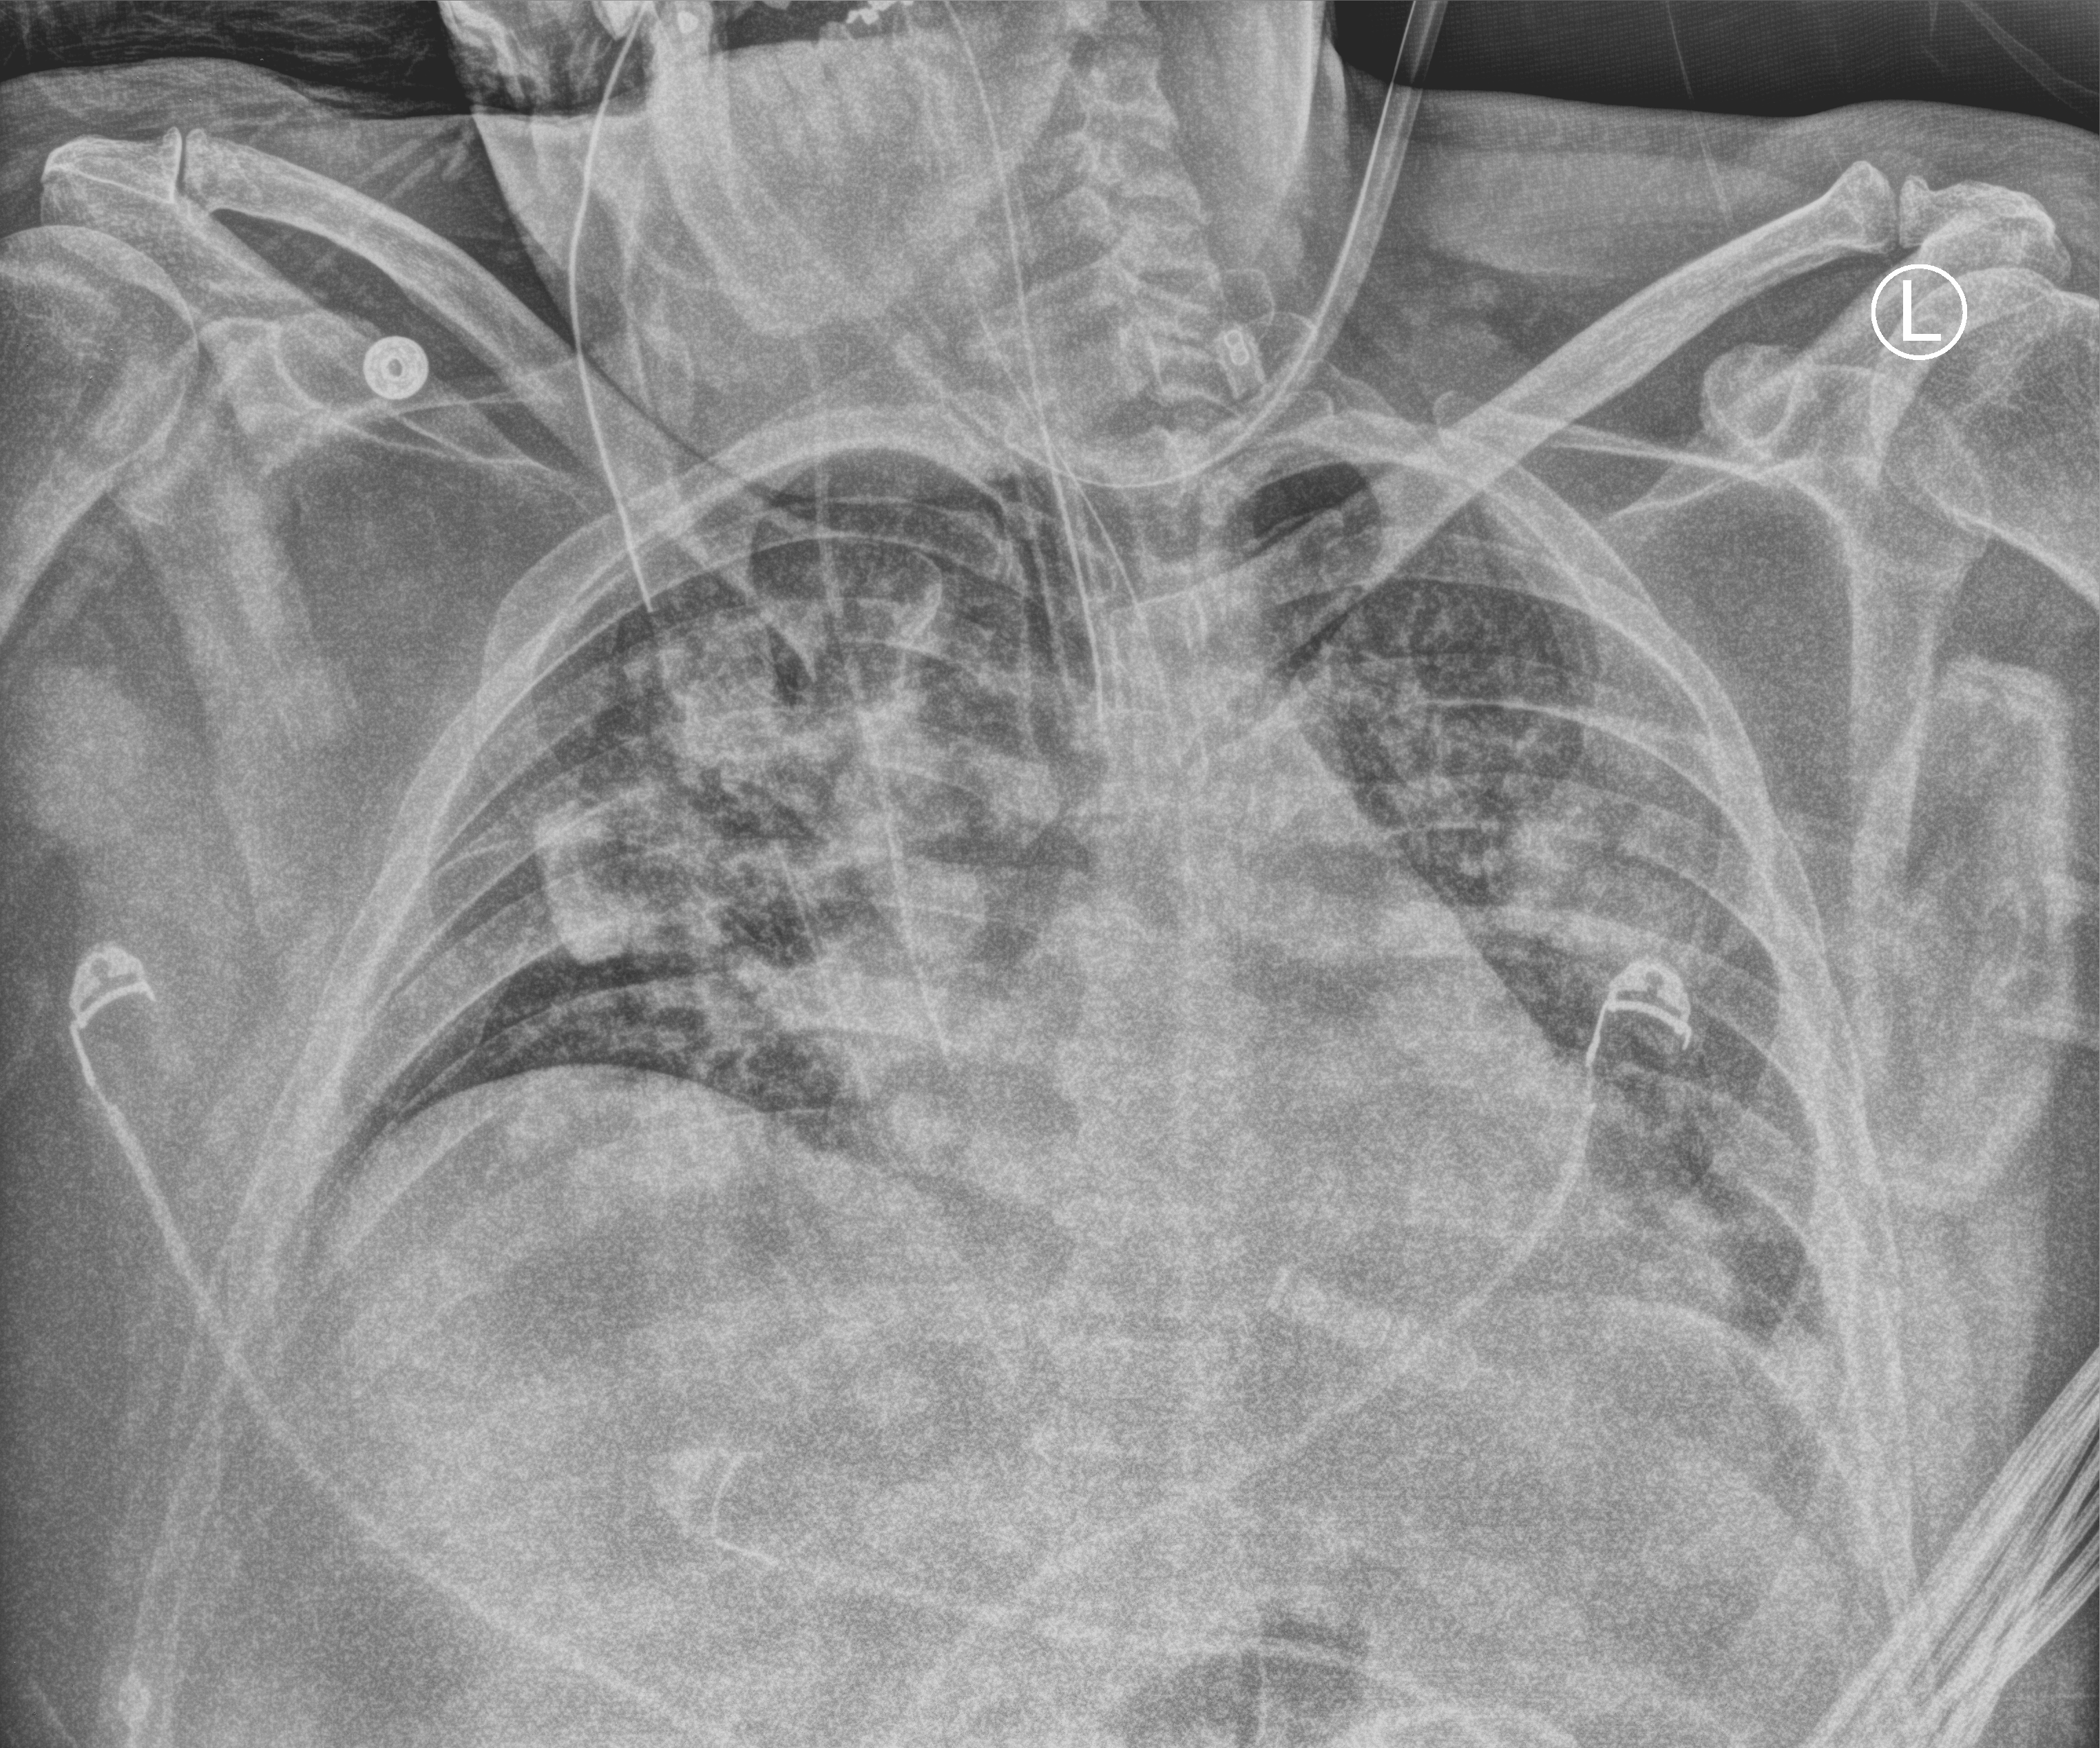
Portable chest radiograph; anteroposterior (AP) projection. Male patient hospitalised with COVID-19, age 18–59 years.
Admission-level facts for this patient (not findings on this image; timing relative to this image not recorded): chronic kidney disease (admission record): no; length of hospital stay: 39 days.